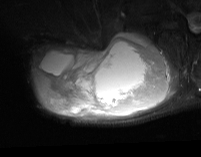
MRI of an extremity soft-tissue mass, one axial slice. Slice 45 of 74 in the series (ordered by position). STIR. MR volume resampled by the dataset authors to the PET/CT grid (not the native acquisition matrix). 3.27 mm slice thickness. 201 × 157 image matrix, field of view 196 × 153 mm. Male patient. Case-level facts recorded for this patient, not image findings: histological type: pleiomorphic spindle cell undifferentiated; grade: high; site of the primary tumour: right parascapusular.
Annotated regions visible in this slice (expert contour drawn on MRI and transferred to this co-registered scan by the dataset authors):
- gross tumour volume including surrounding oedema: bounding box (x1, y1, x2, y2) in pixels: (33, 29, 178, 120)
- gross tumour volume (mass): (35, 32, 171, 117)